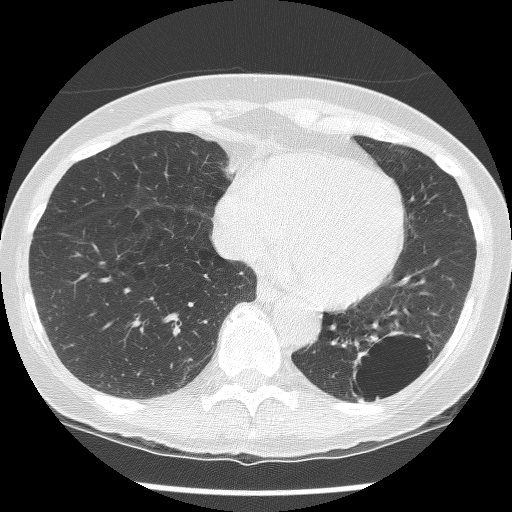
Axial slice from a low-dose chest CT screening exam. Second annual screen. Lung window (W 1500 / L -600 HU). 120 kVp. Slice 92 of 136 in the series. 512 × 512 image matrix, field of view 300 × 300 mm. Female participant, aged 61 years at enrolment. Current smoker at enrolment.
- Lesion marked by an expert reader, bounding box (x1, y1, x2, y2) in pixels: (331, 324, 436, 415).
- The screening reader recorded 2 non-calcified nodules or masses ≥4 mm on this exam (left lower lobe, left lower lobe); which of them this box marks is not recorded.
- Official screen result: positive, no significant change: stable abnormalities potentially related to lung cancer, unchanged since the prior screening exam.
- Participant outcome: lung cancer diagnosed 585 days after this screen (after the third annual screen) — non-small cell carcinoma, left lower lobe, poorly differentiated (G3), stage IB (AJCC 6th edition), 100 mm at pathology.